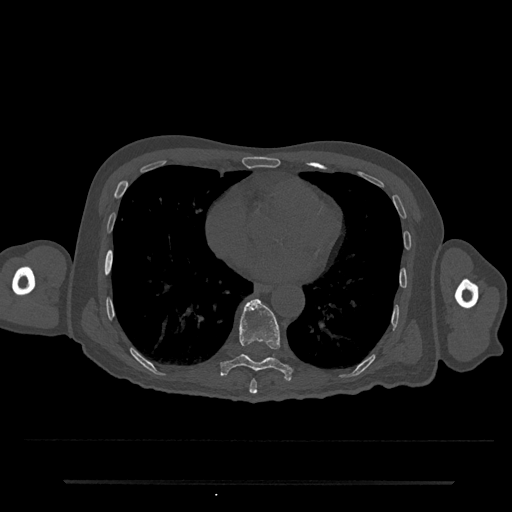
CT including the spine, one axial slice. Slice 368 of 797 in the series (ordered by position). Reconstruction kernel Br40s/3. Bone window (W 1800 / L 400 HU). 512 × 512 image matrix, field of view 427 × 427 mm. Patient: male, 74 years. From the clinical record (not read from this slice): primary cancer: prostate.
Outlined on this slice (semi-automatic segmentation, software-assisted and operator-edited):
- T8 vertebra: bounding box [x1, y1, x2, y2] px = [249, 379, 258, 394]
- T9 vertebra: [220, 299, 294, 380]